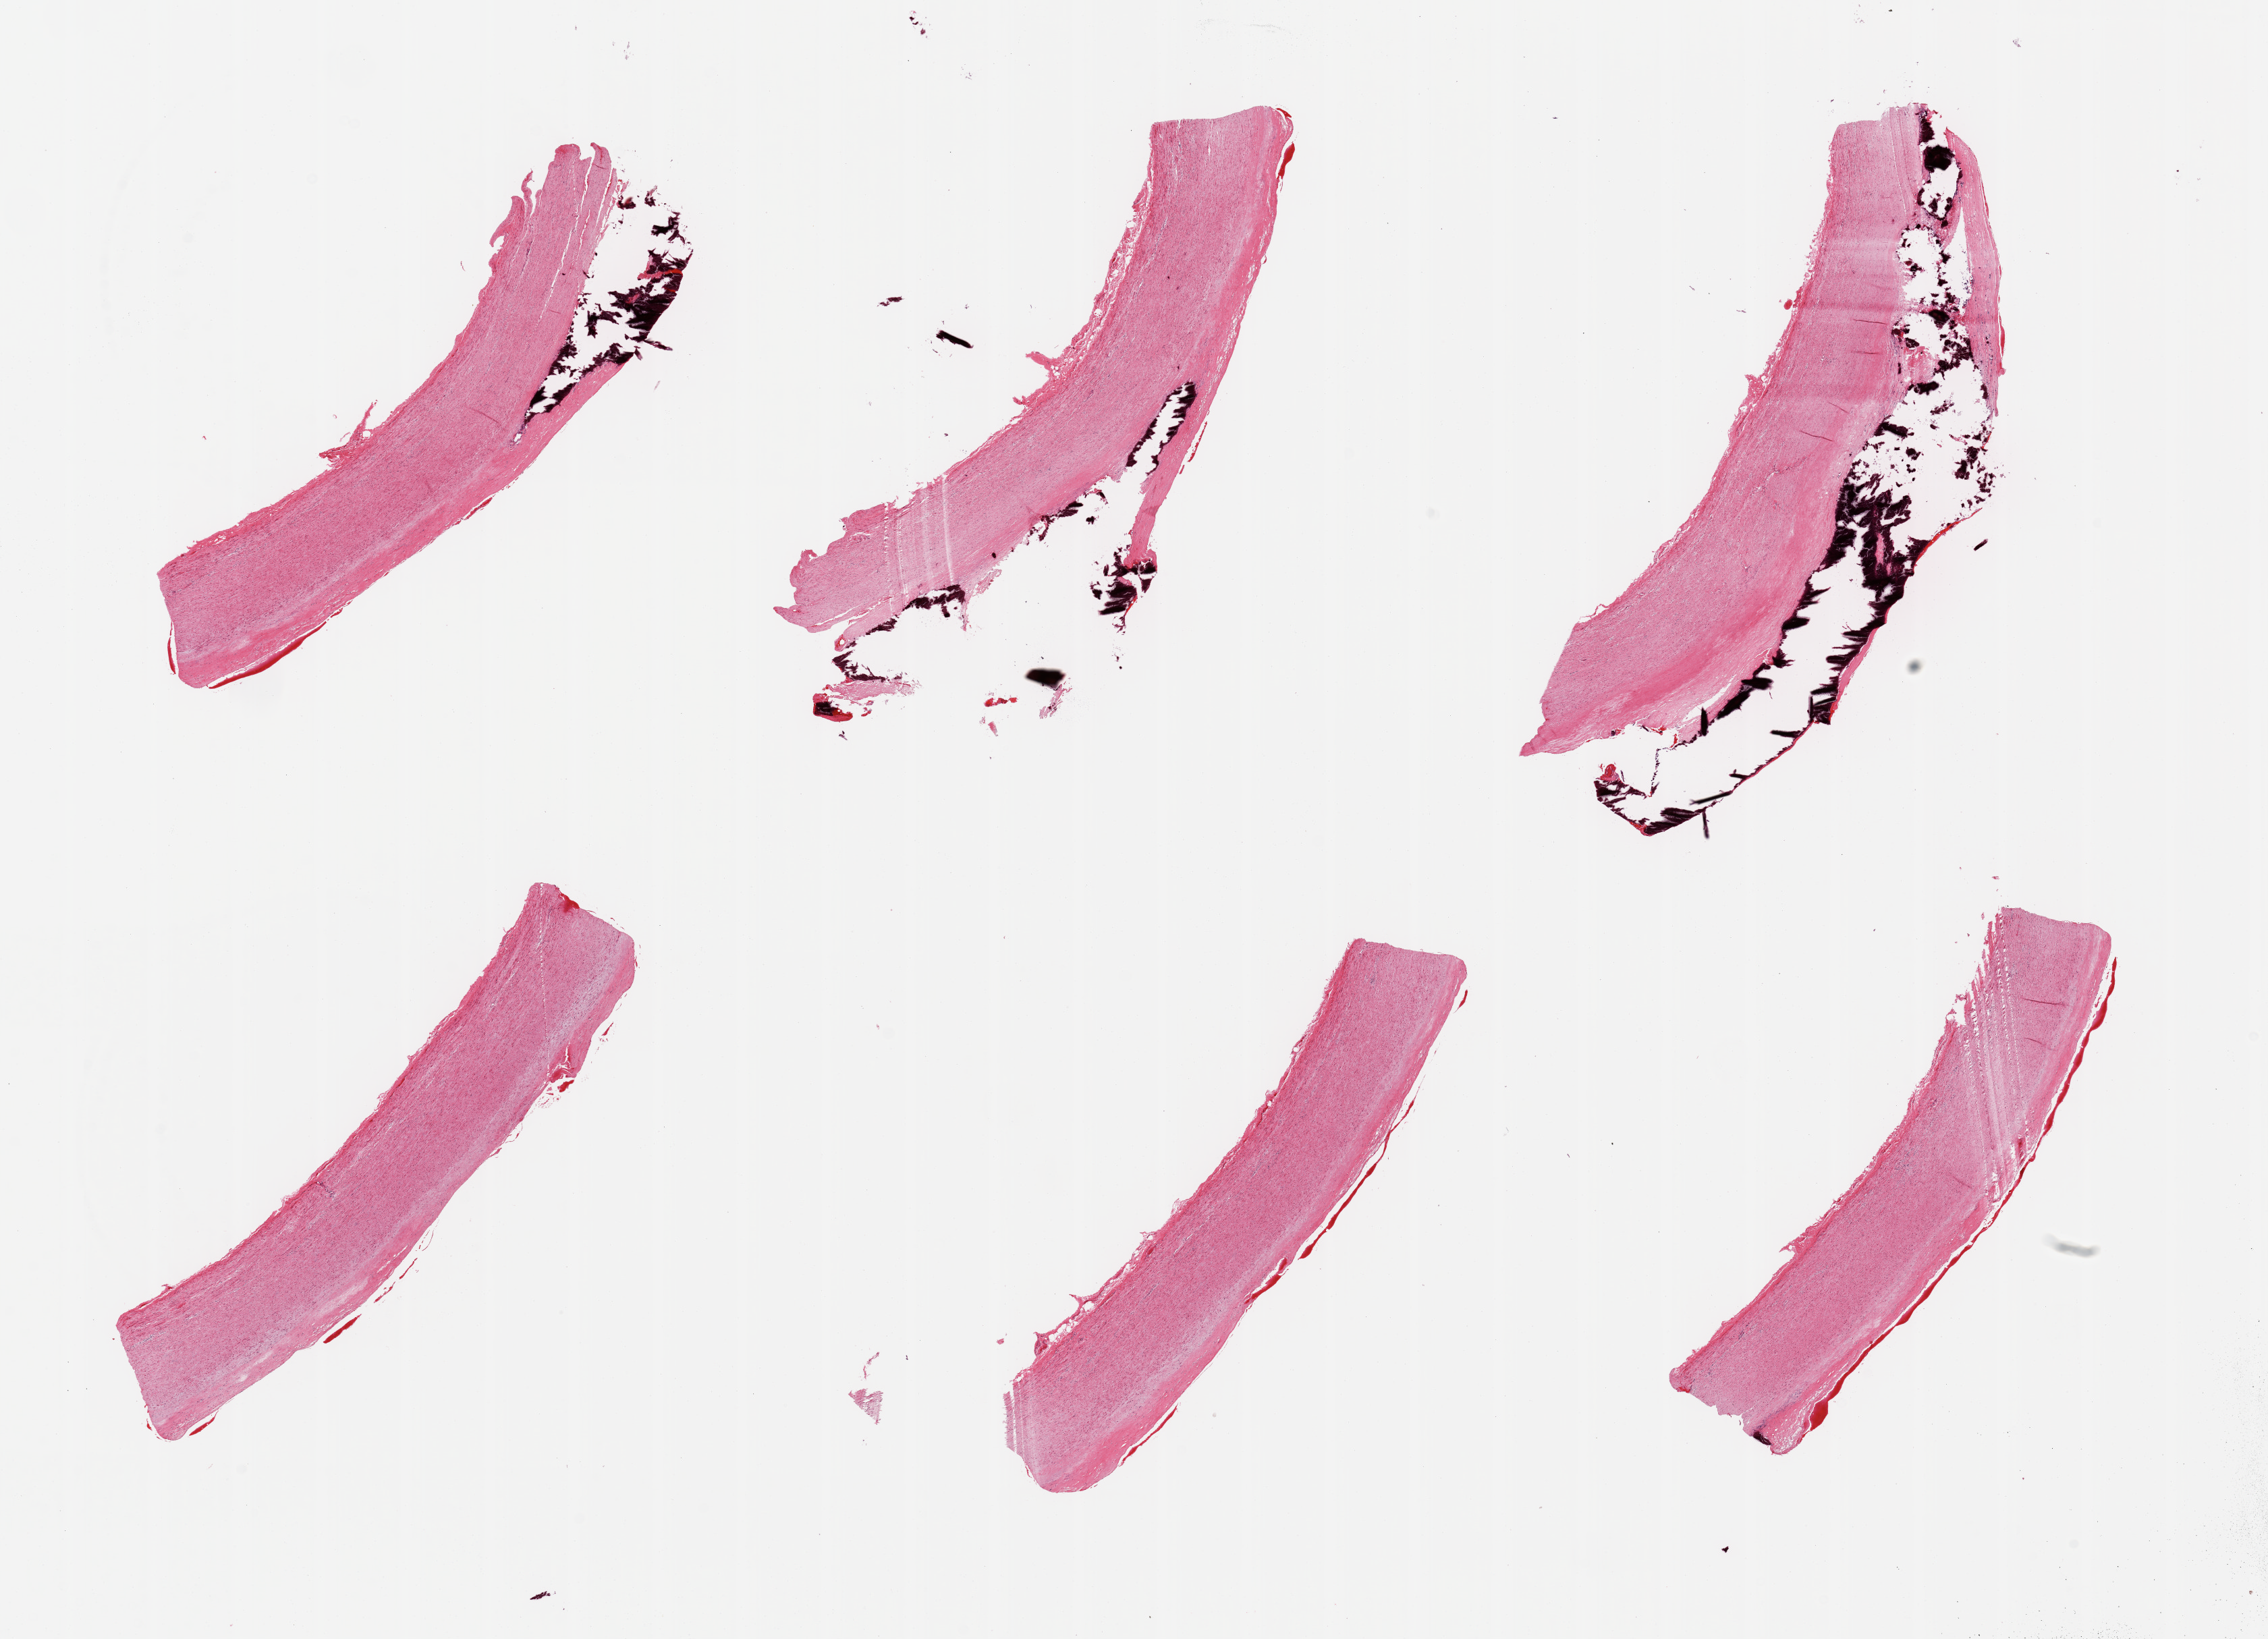
H&E whole-slide image, whole scanned area (about 26.6 x 19.2 mm, from a 20x scan) shown as a low-resolution overview, PAXgene-fixed paraffin-embedded (PFPE) section, sampled site (target tissue): aorta, donor tissue sample. Male donor.
Pathologist's review note for this sample: 6 pieces; calcific atherosclerosis.